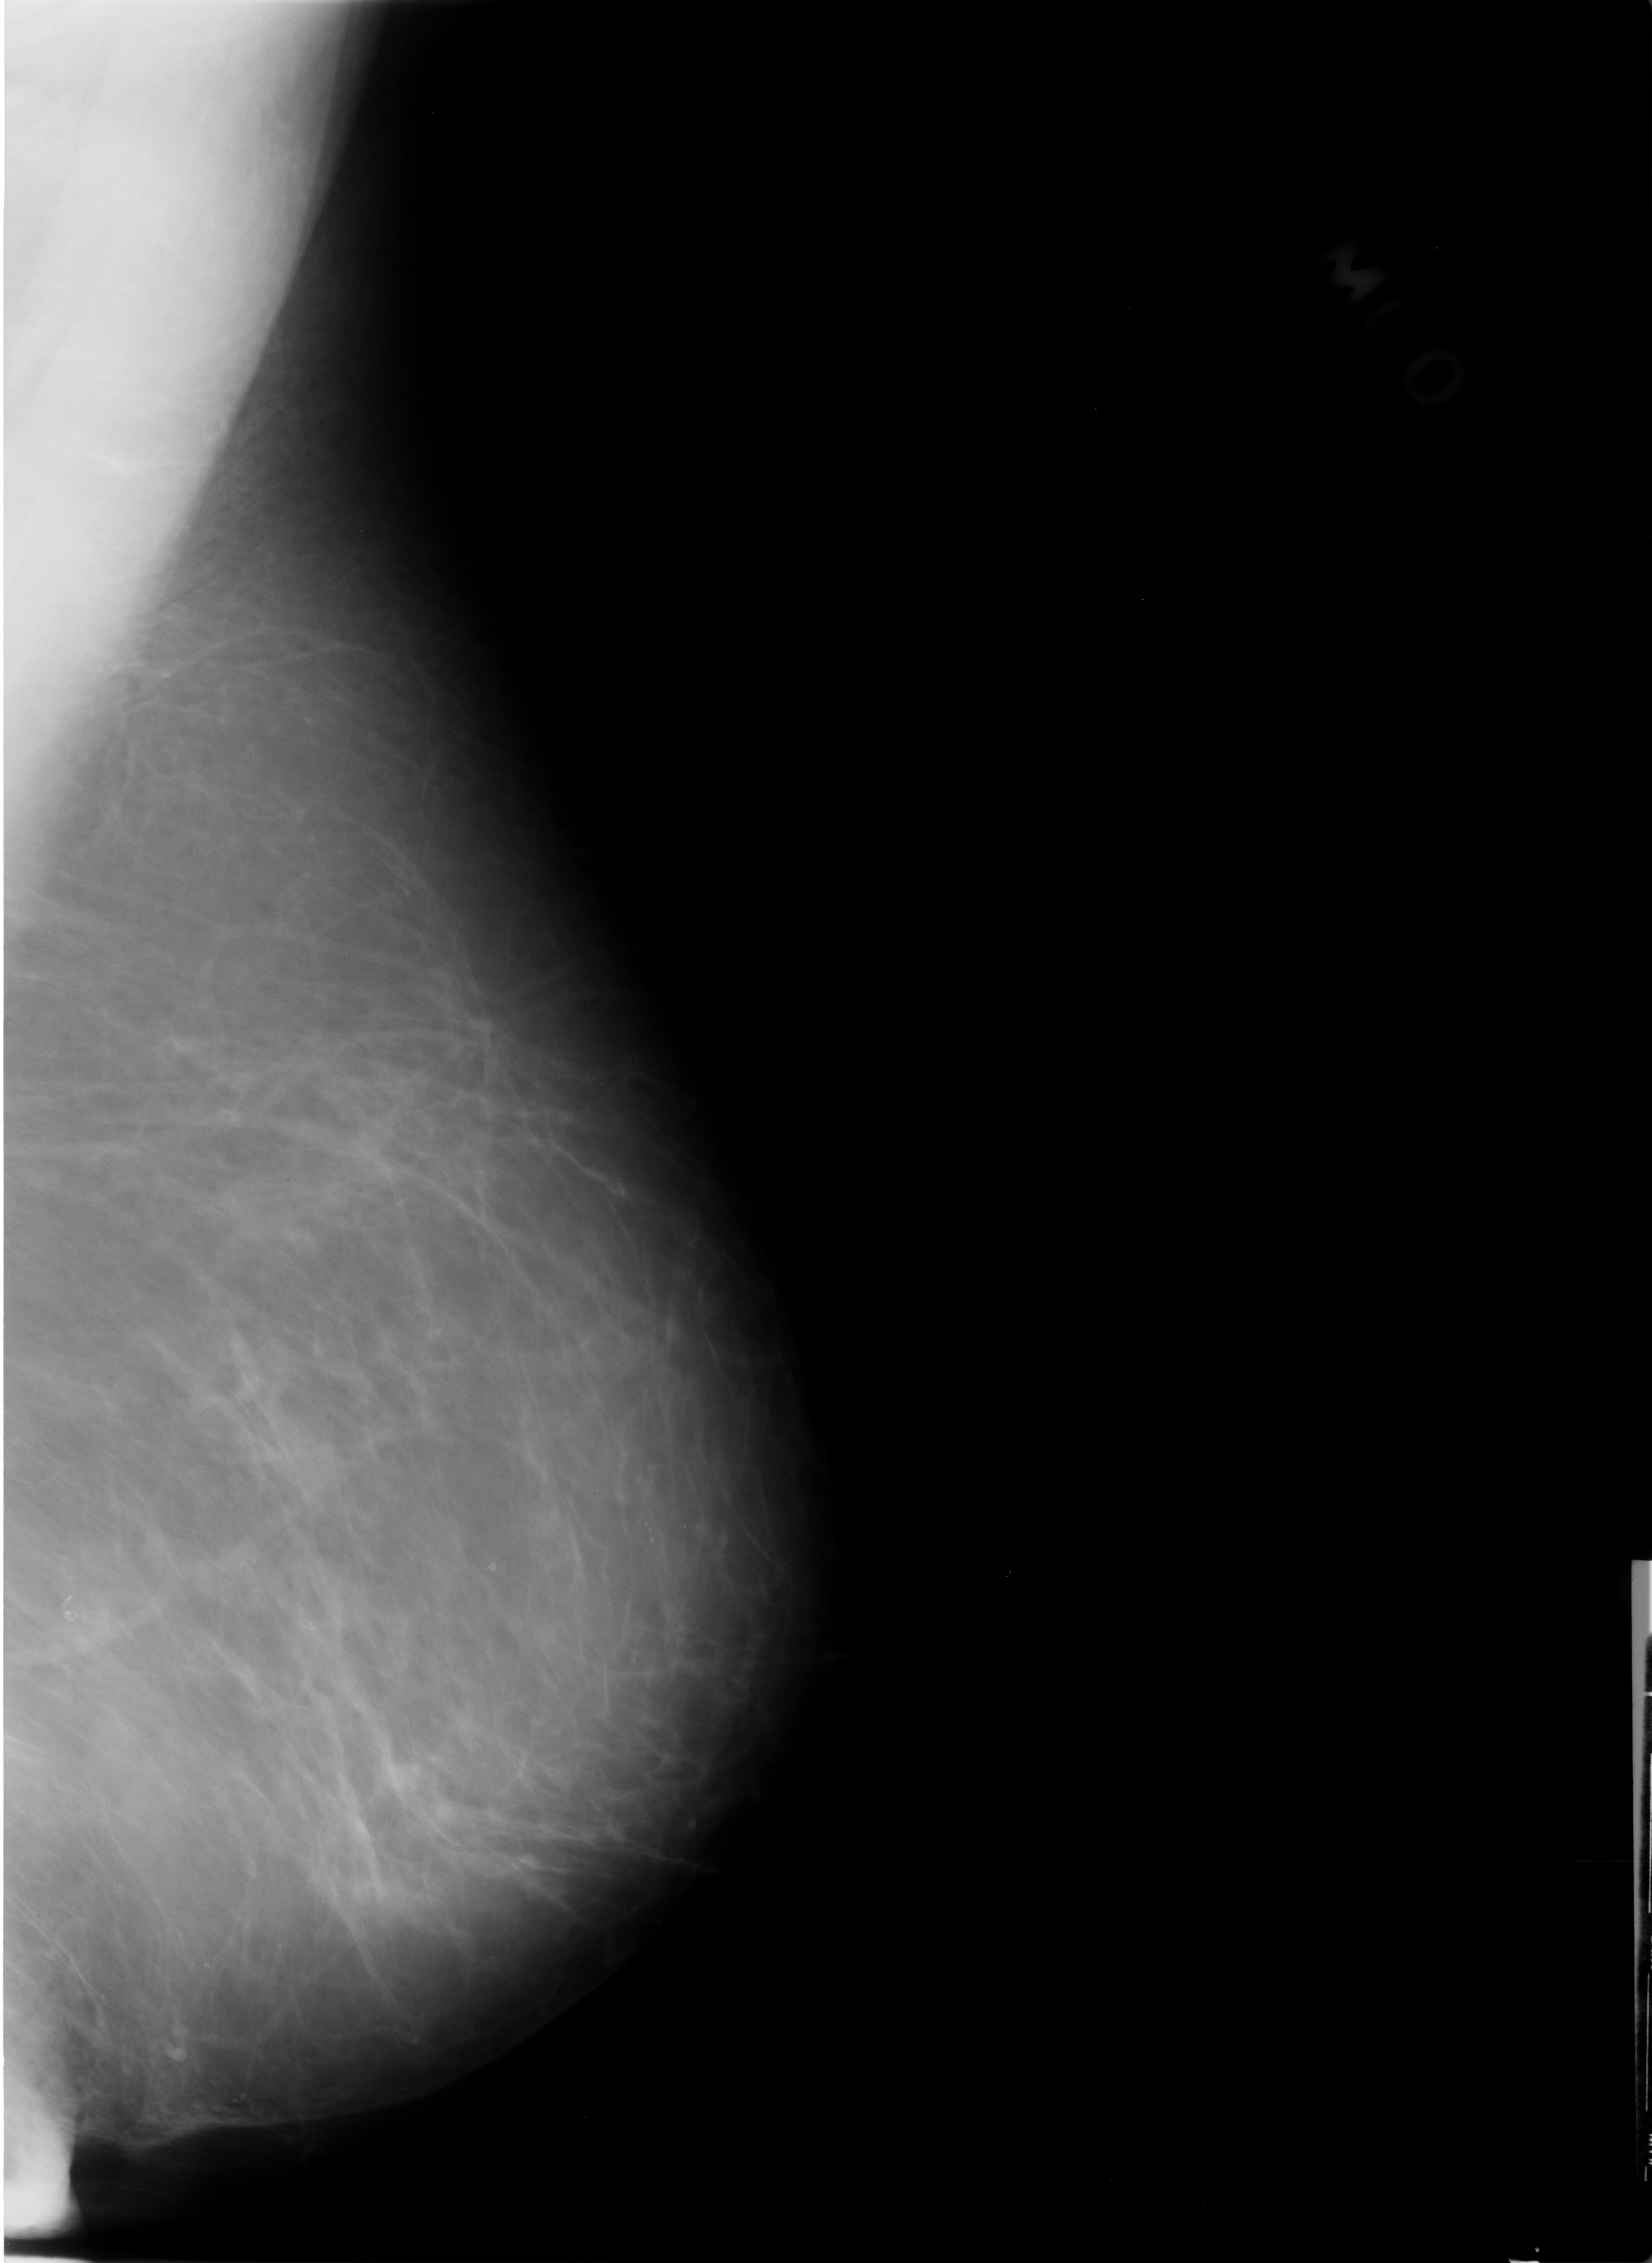
Mammogram (digitized film); left breast; MLO view; 1652 × 2263 image matrix.
Expert-marked regions of interest on this image (one box per marked abnormality):
- calcifications, morphology pleomorphic, distribution clustered; BI-RADS assessment category 4; pathology result (as recorded, not read from the image): benign: bounding box [x1, y1, x2, y2] px = [40, 1554, 127, 1669]